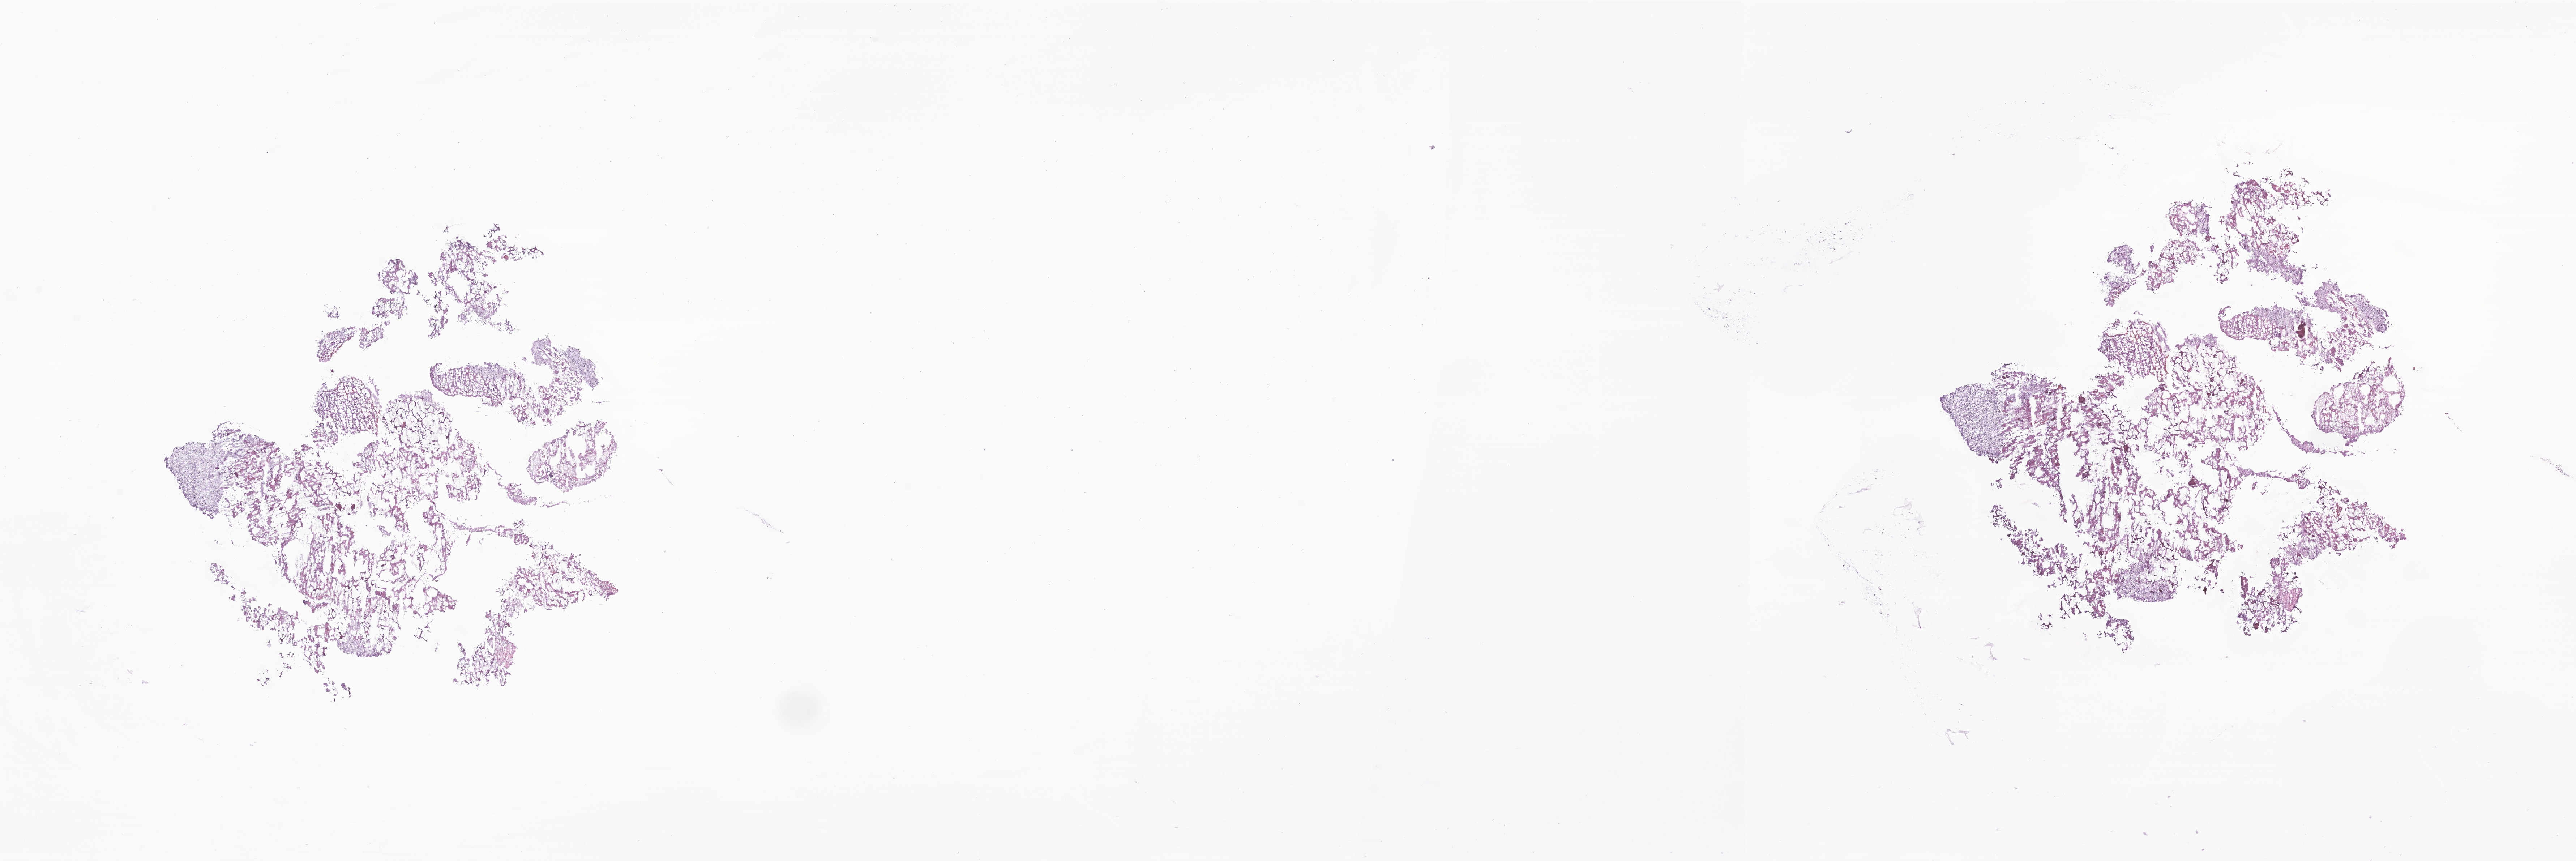
Hematoxylin and eosin (H&E) whole-slide image of tumor tissue from the brain — low-resolution overview of the scanned area, about 30.0 x 10.0 mm. Cryosection (OCT / tissue freezing medium). Patient male; age 258 months (21 years 6 months).
Diagnosis: Glioma, malignant.